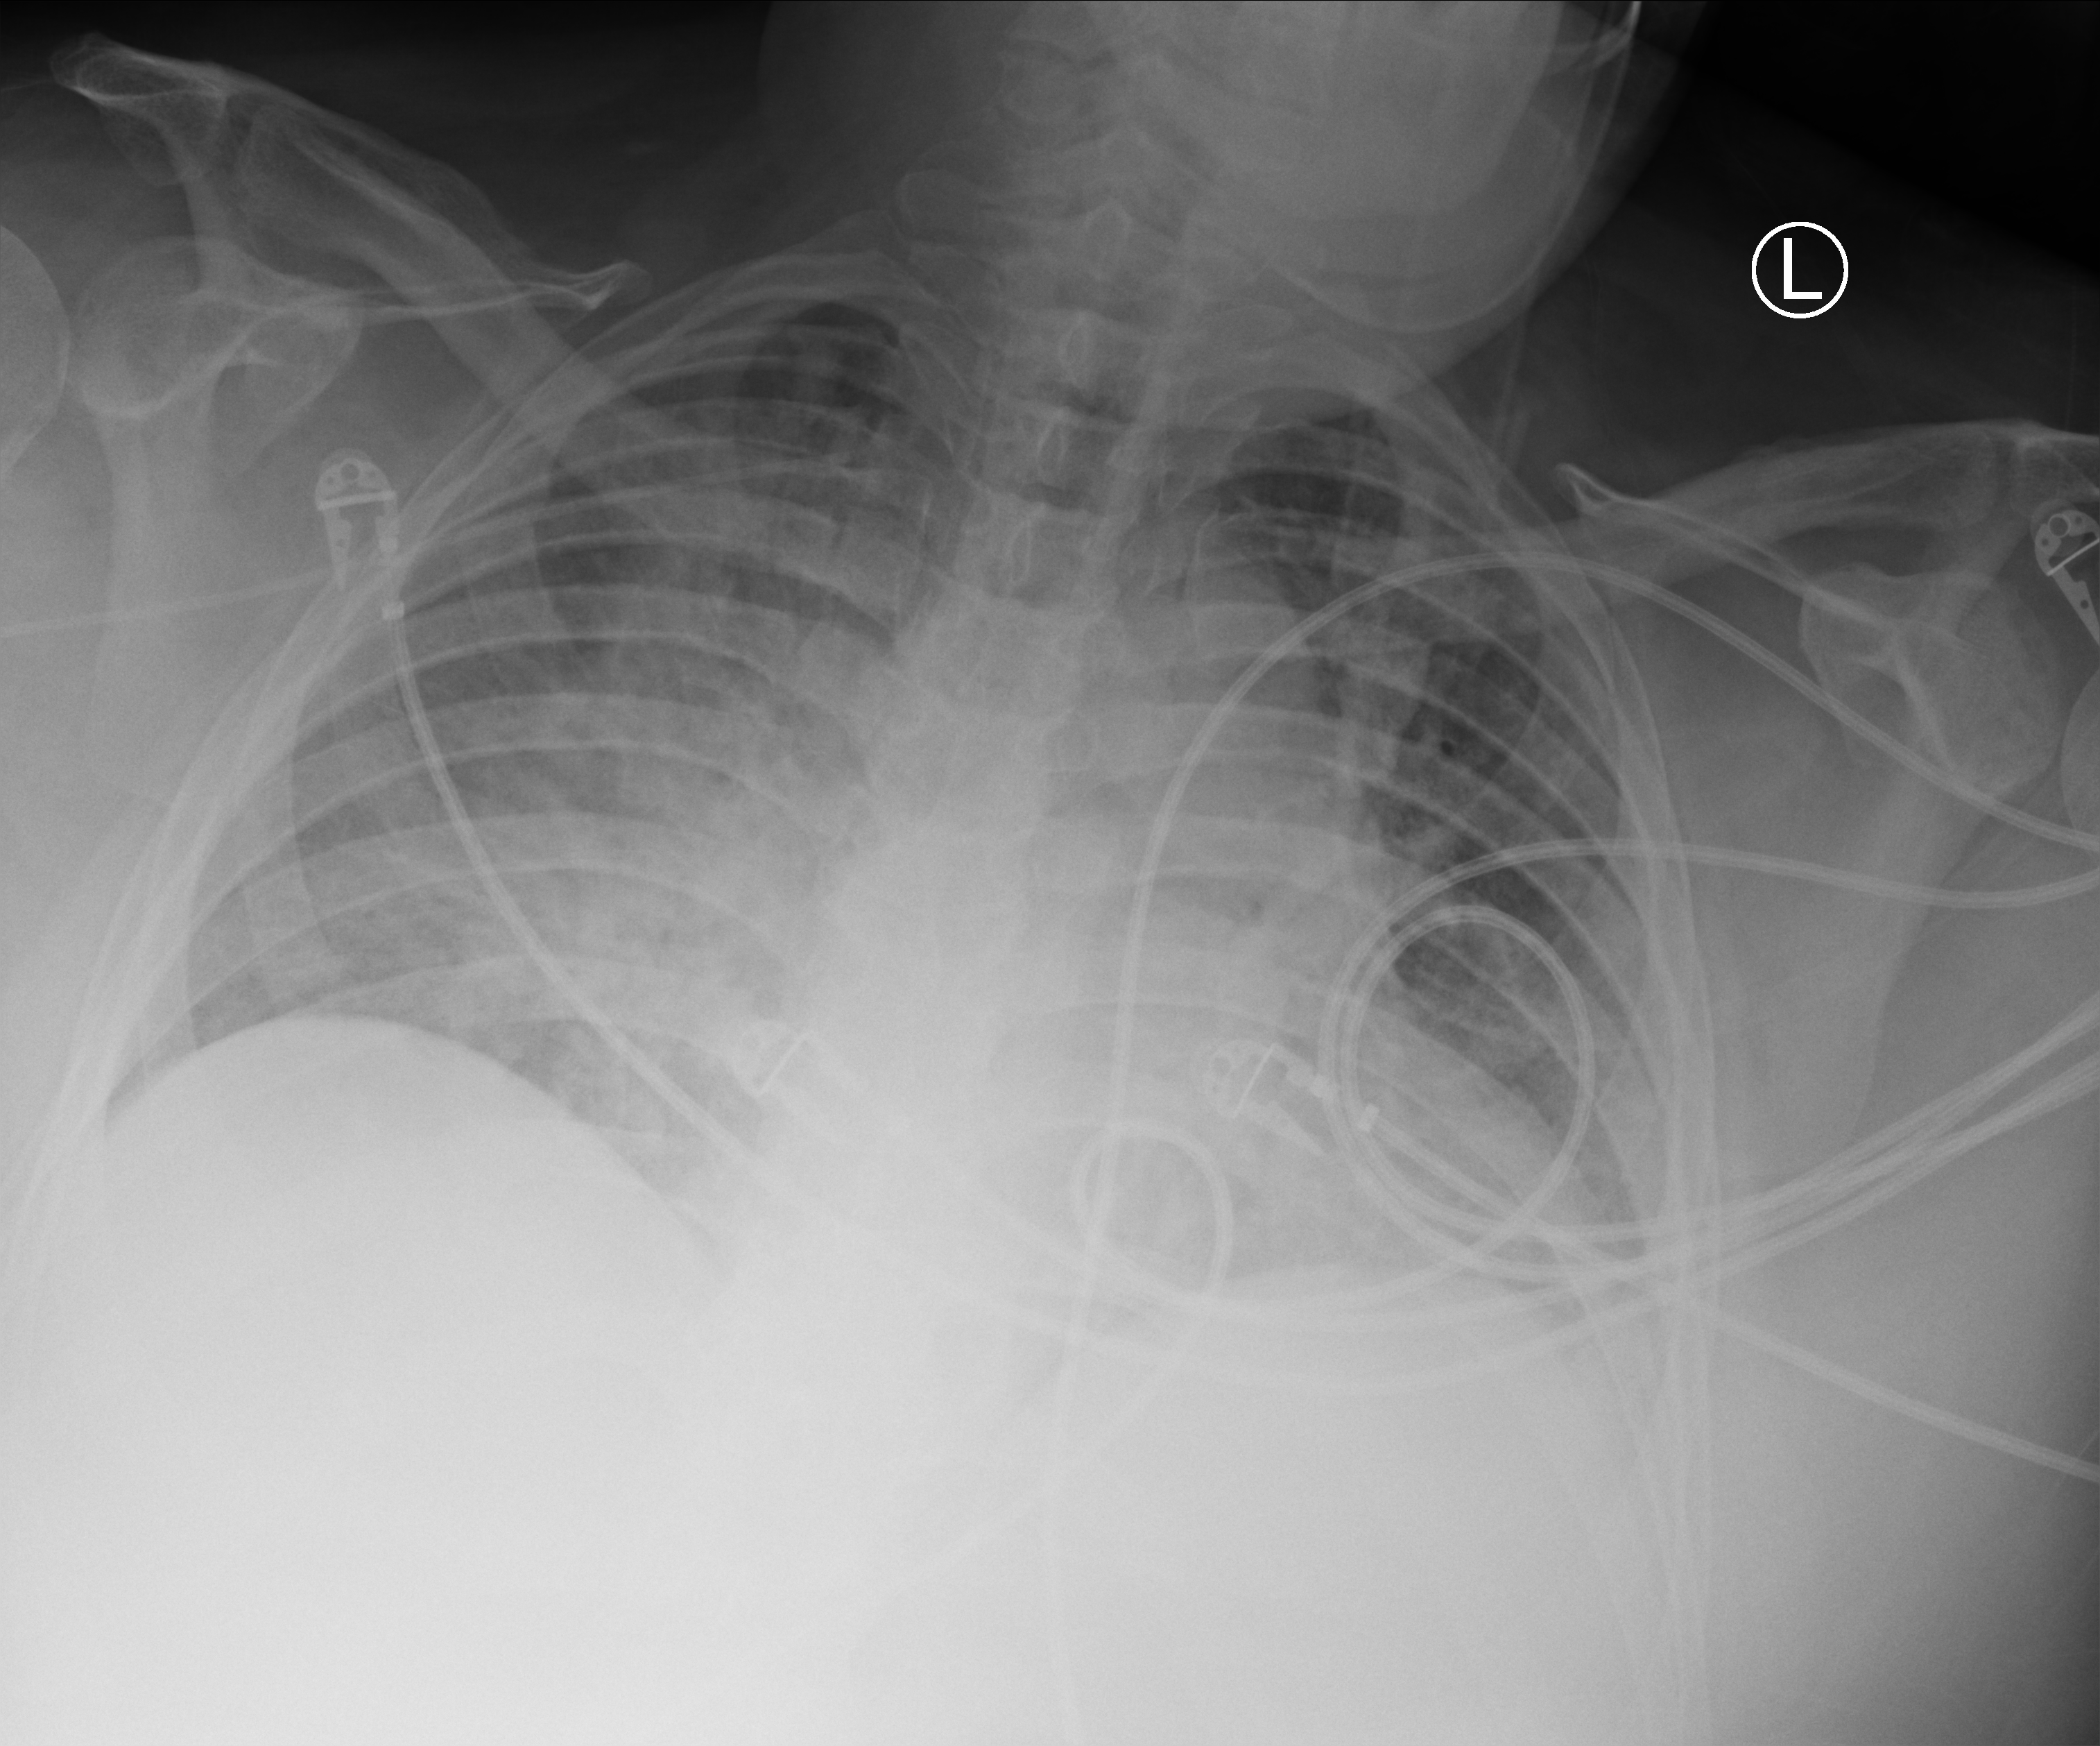
Bedside chest radiograph (computed radiography), anteroposterior (AP) projection. Male patient hospitalised with COVID-19, age 18–59 years.
Admission-level facts for this patient (not findings on this image; timing relative to this image not recorded):
- diabetes (admission record): yes
- hypertension (admission record): no